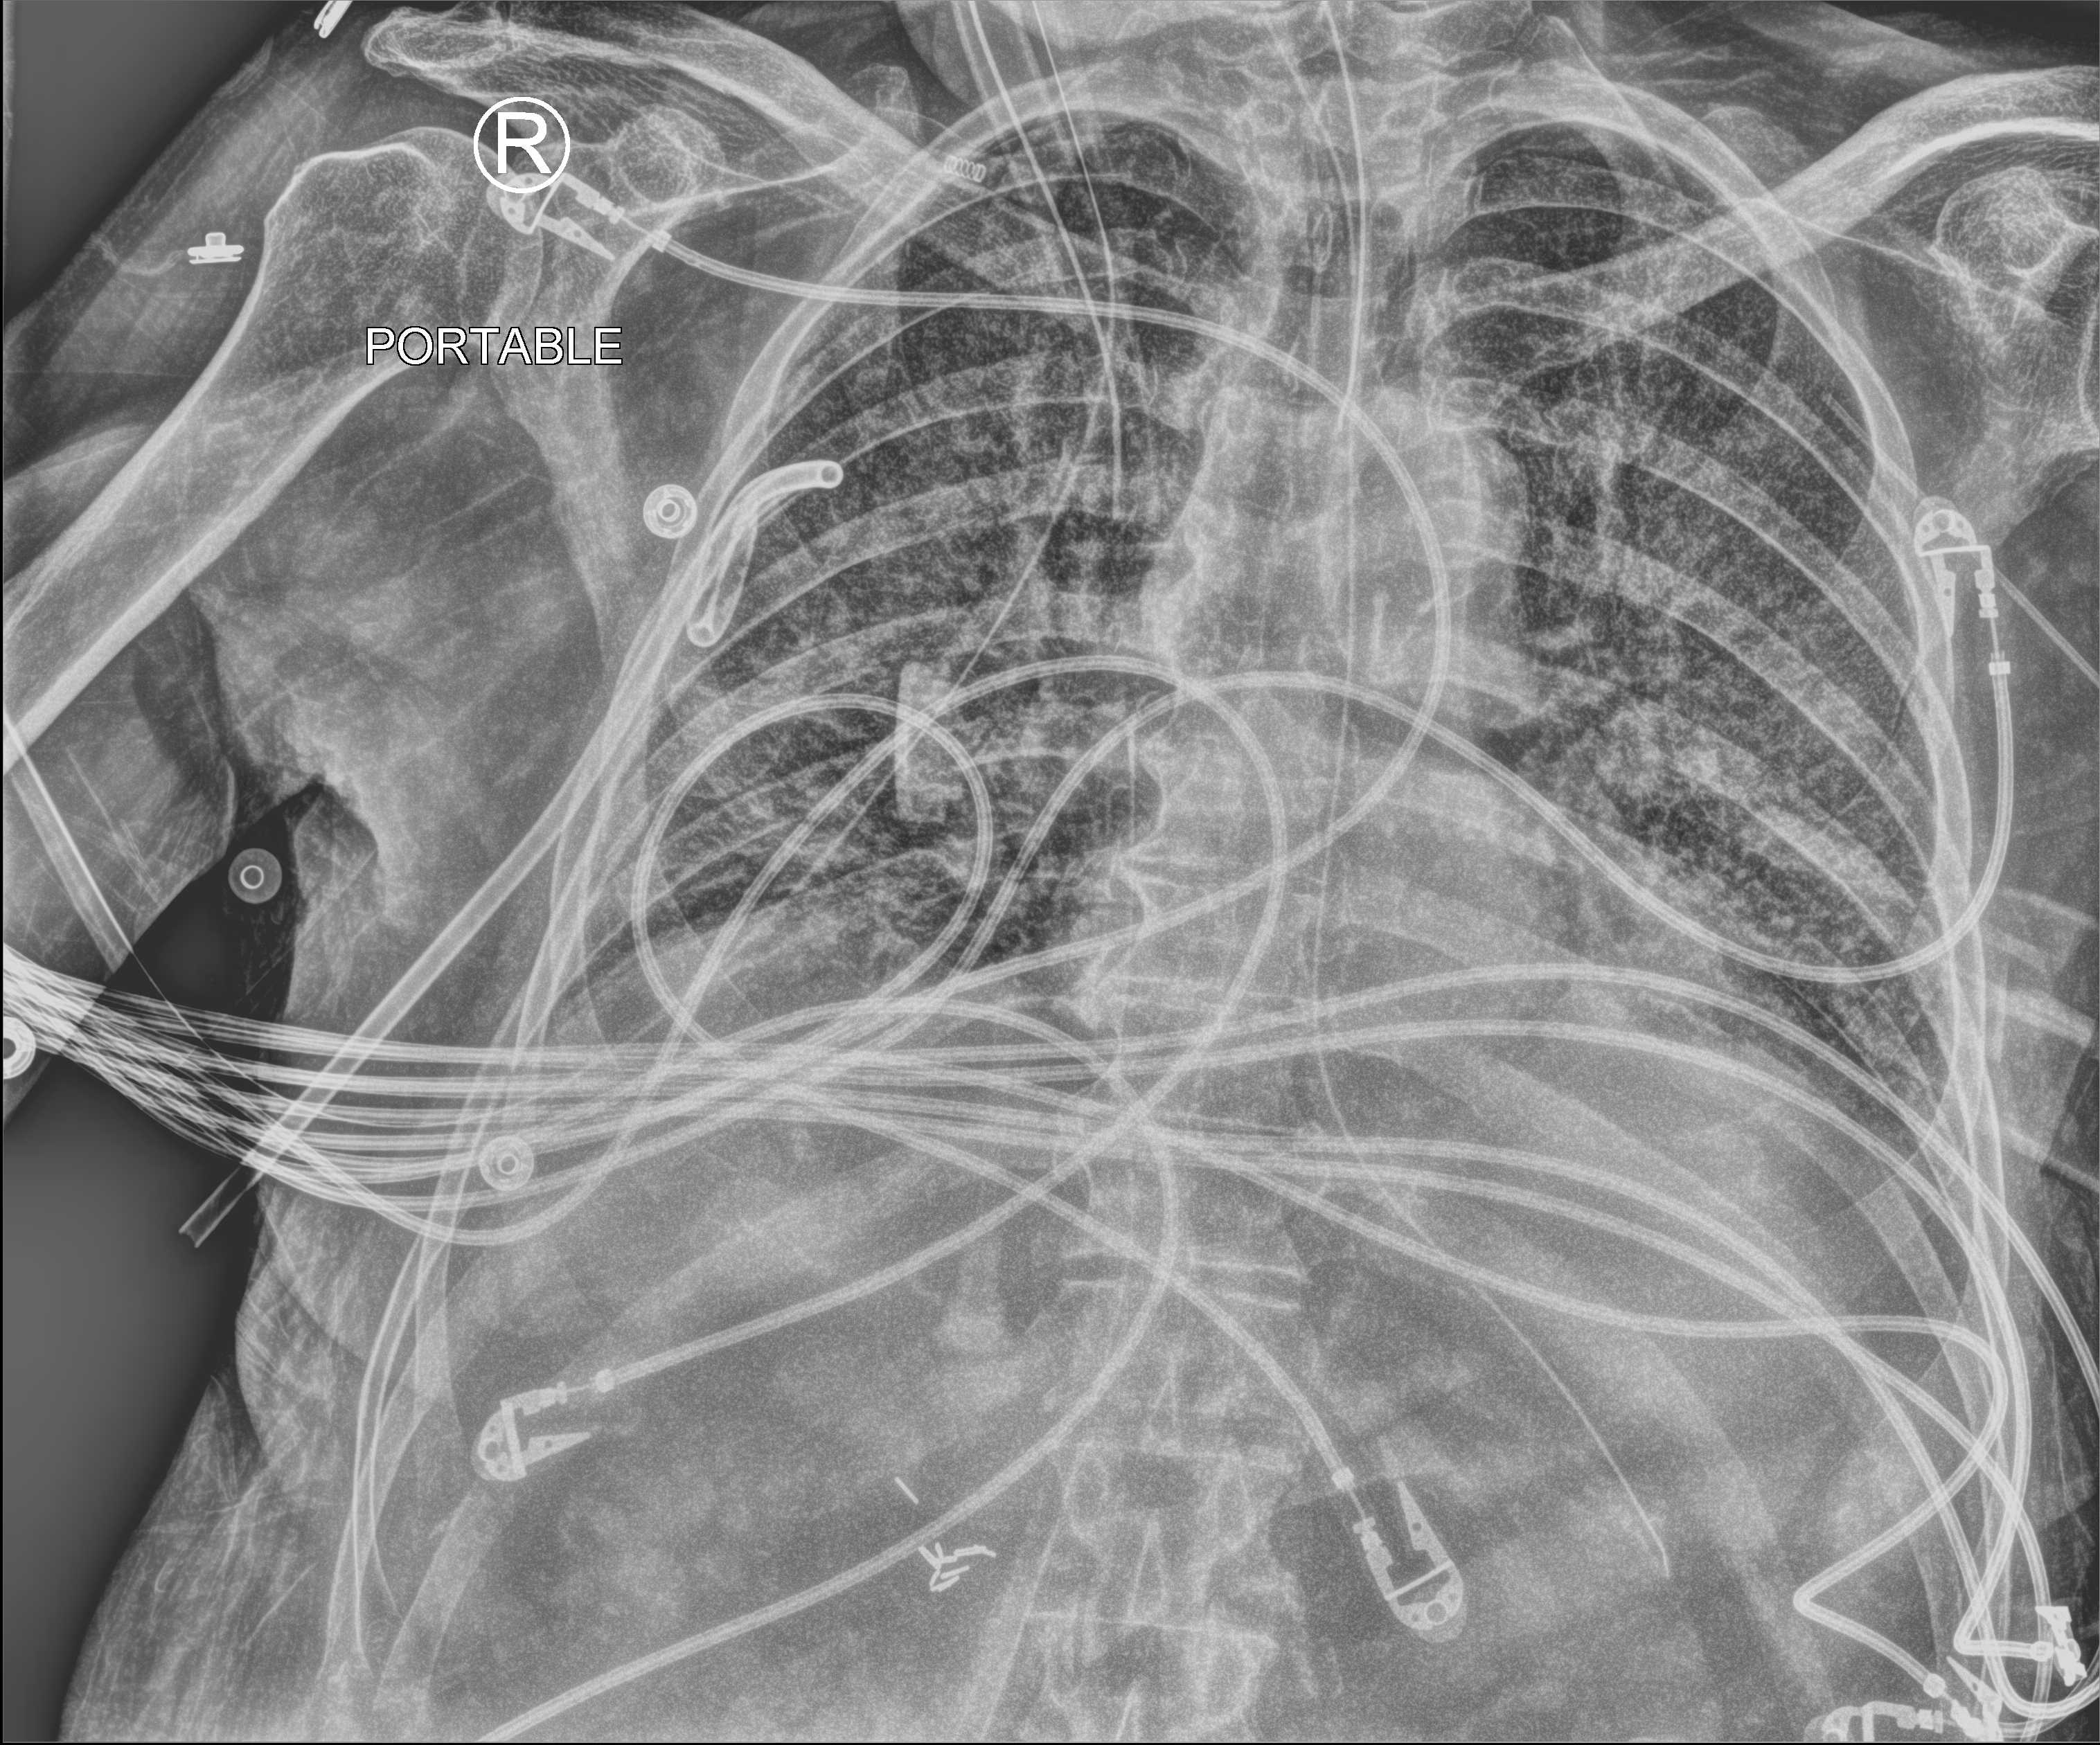
Bedside chest radiograph (computed radiography), anteroposterior (AP) projection. Male patient hospitalised with COVID-19, age 75–90 years.
From the hospital-stay record, not from the radiograph (when in the stay this image was taken is not recorded):
- admitted to intensive care during this hospital stay: yes
- other chronic lung disease (admission record): no